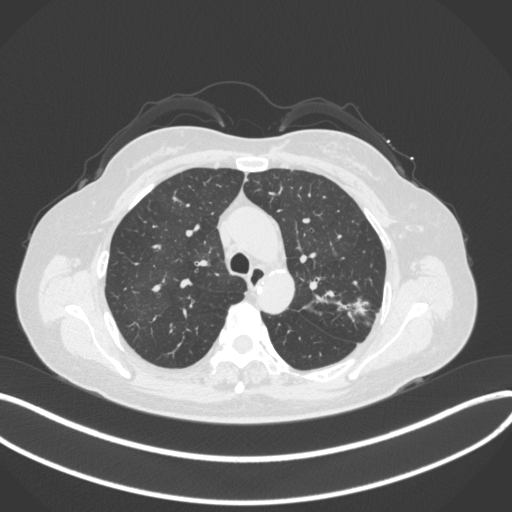
Chest CT, one axial slice. Slice 245 of 330 in the series (ordered by position). 120 kVp. Lung window (W 1500 / L -600 HU). 1 mm slice thickness. 512 × 512 image matrix, field of view 400 × 400 mm. Patient: female, 60 years. Case-level facts recorded for this patient, not image findings: clinical TNM (as recorded): T1c N0 M0.
Annotated regions visible in this slice (bounding box drawn by a radiologist):
- lung tumour (recorded histology: adenocarcinoma): bounding box <339,289,373,320> (left, top, right, bottom; pixels)